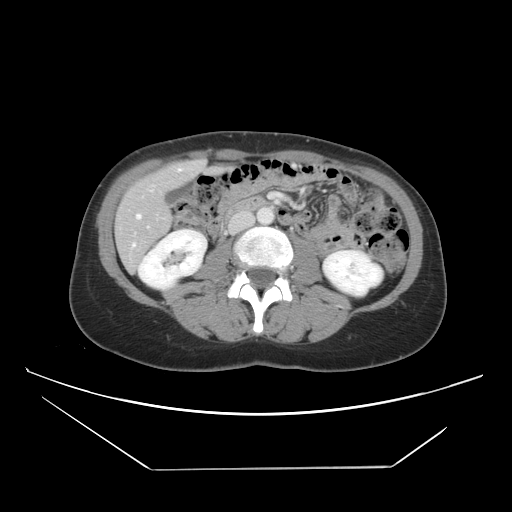
Contrast-enhanced abdominal CT, one axial slice; position 15 of 42 along the scan axis; intravenous contrast given; soft-tissue window (W 400 / L 40 HU); 5 mm slice thickness; 512 × 512 image matrix, field of view 399 × 399 mm. Female patient, age 52 years. From the clinical record (not read from this slice): diagnosis: colorectal cancer liver metastases, imaged before liver resection; multiple liver metastases: yes; largest metastasis: 5.5 cm; disease in both lobes: yes.
Annotated regions visible in this slice (manually delineated by an expert):
- hepatic veins: box from (x=132, y=163) to (x=202, y=247) px
- liver: (x=117, y=161)–(x=212, y=269)
- planned liver remnant (the part of the liver to remain after resection): (x=122, y=161)–(x=209, y=216)
- portal vein (with intrahepatic branches): (x=147, y=194)–(x=270, y=228)